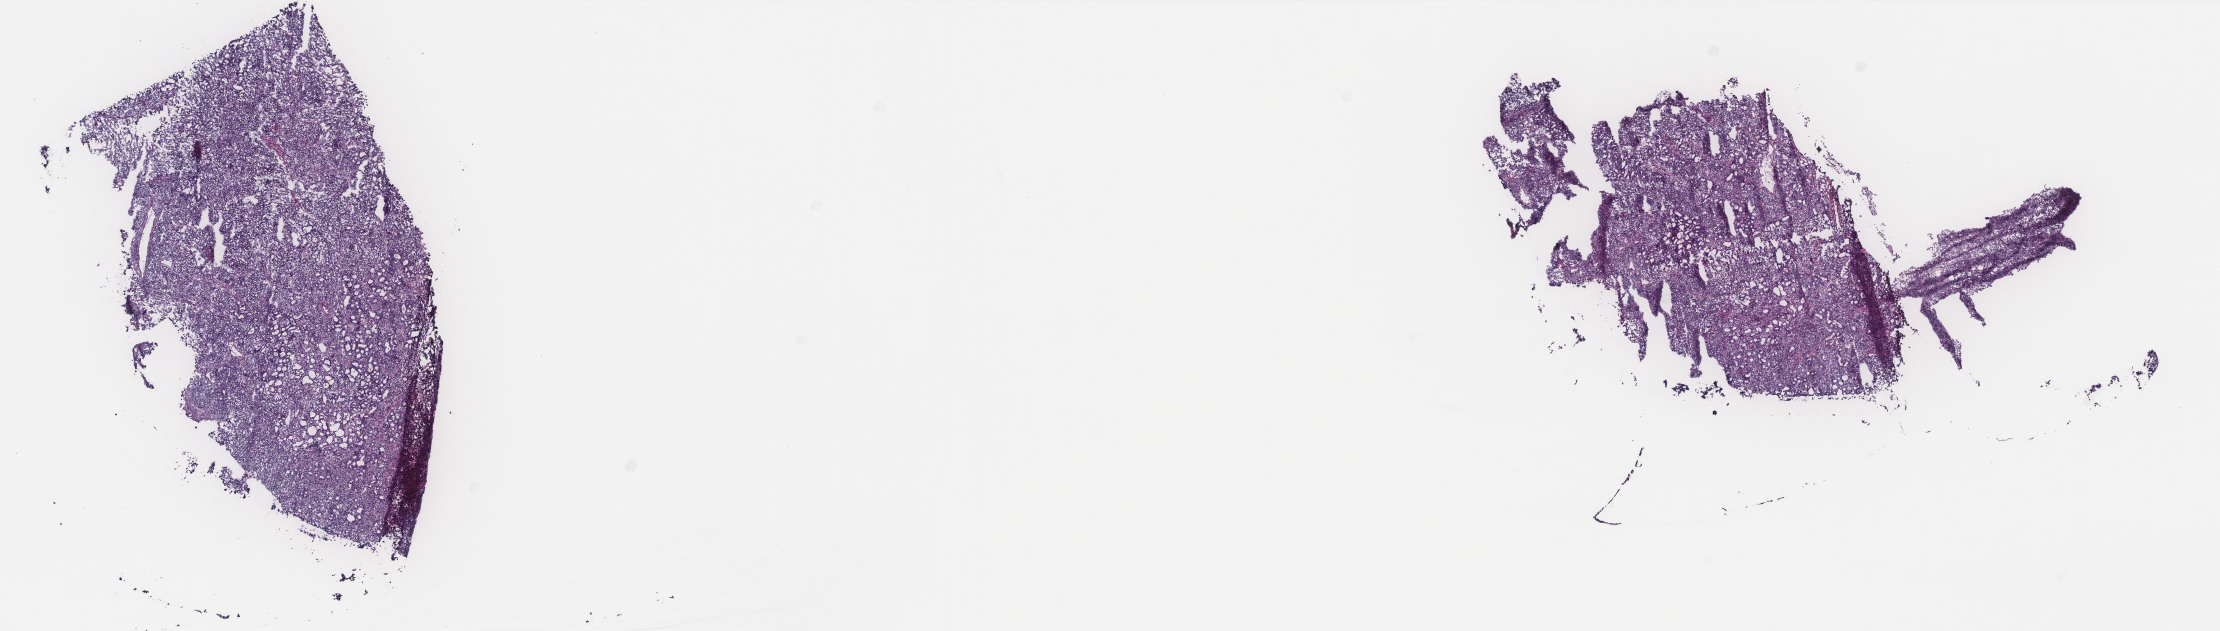
Whole-slide histology image, H&E, a low-resolution overview of the entire scanned area, about 17.8 x 5.1 mm (from a 40x scan); frozen section; uterus, primary tumour sample. Female patient; age at initial diagnosis 47 years. Histologic grade: G3 (poorly differentiated). Pathologist review of this section (percent, as recorded): tumour cells 95%, tumour nuclei 97%, normal cells 0%, stromal cells 3%, necrosis 2%. Inflammatory infiltration, as recorded: lymphocyte infiltration 5%, monocyte infiltration 2%, neutrophil infiltration 2%.
• diagnosis: Endometrioid adenocarcinoma, NOS (endometrium)
• FIGO stage: IB